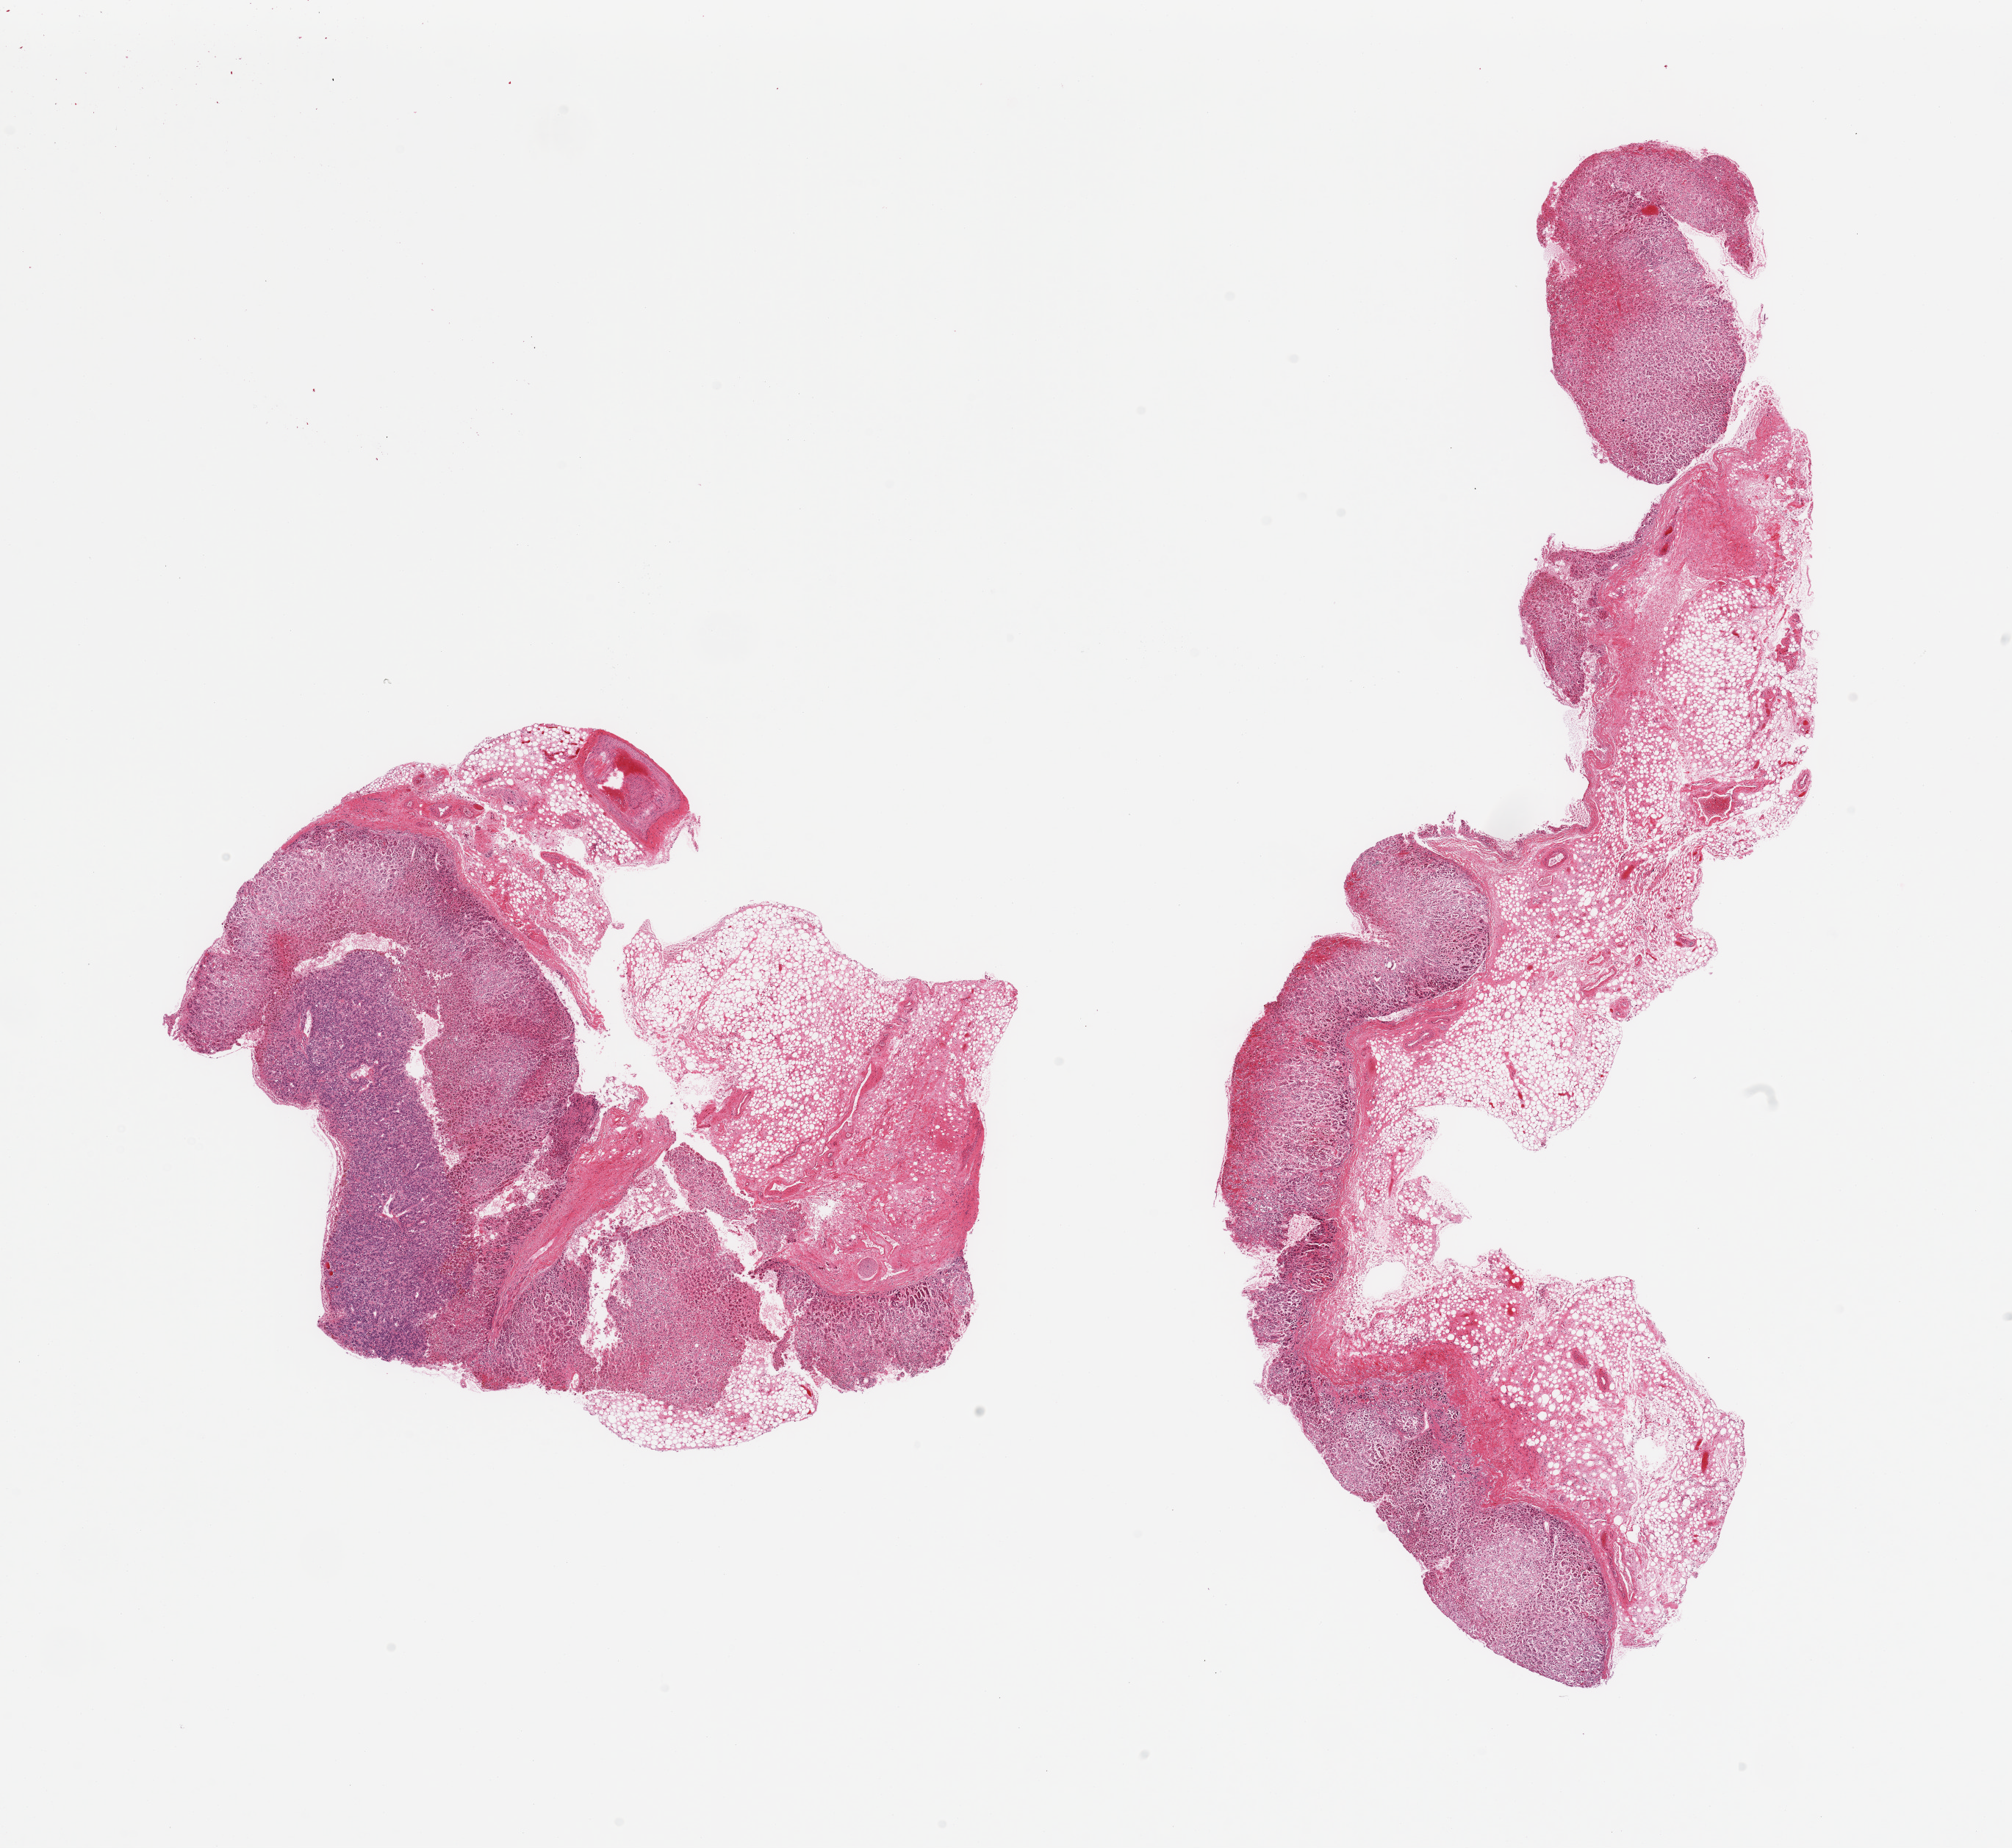
Digitized H&E-stained section, brightfield, low-resolution overview of the scanned area, about 21.7 x 19.9 mm; PAXgene-fixed, paraffin-embedded tissue; section of adrenal gland (target tissue); tissue donor sample.
- pathologist's review note for this sample: 2 pieces; 50% external fat content